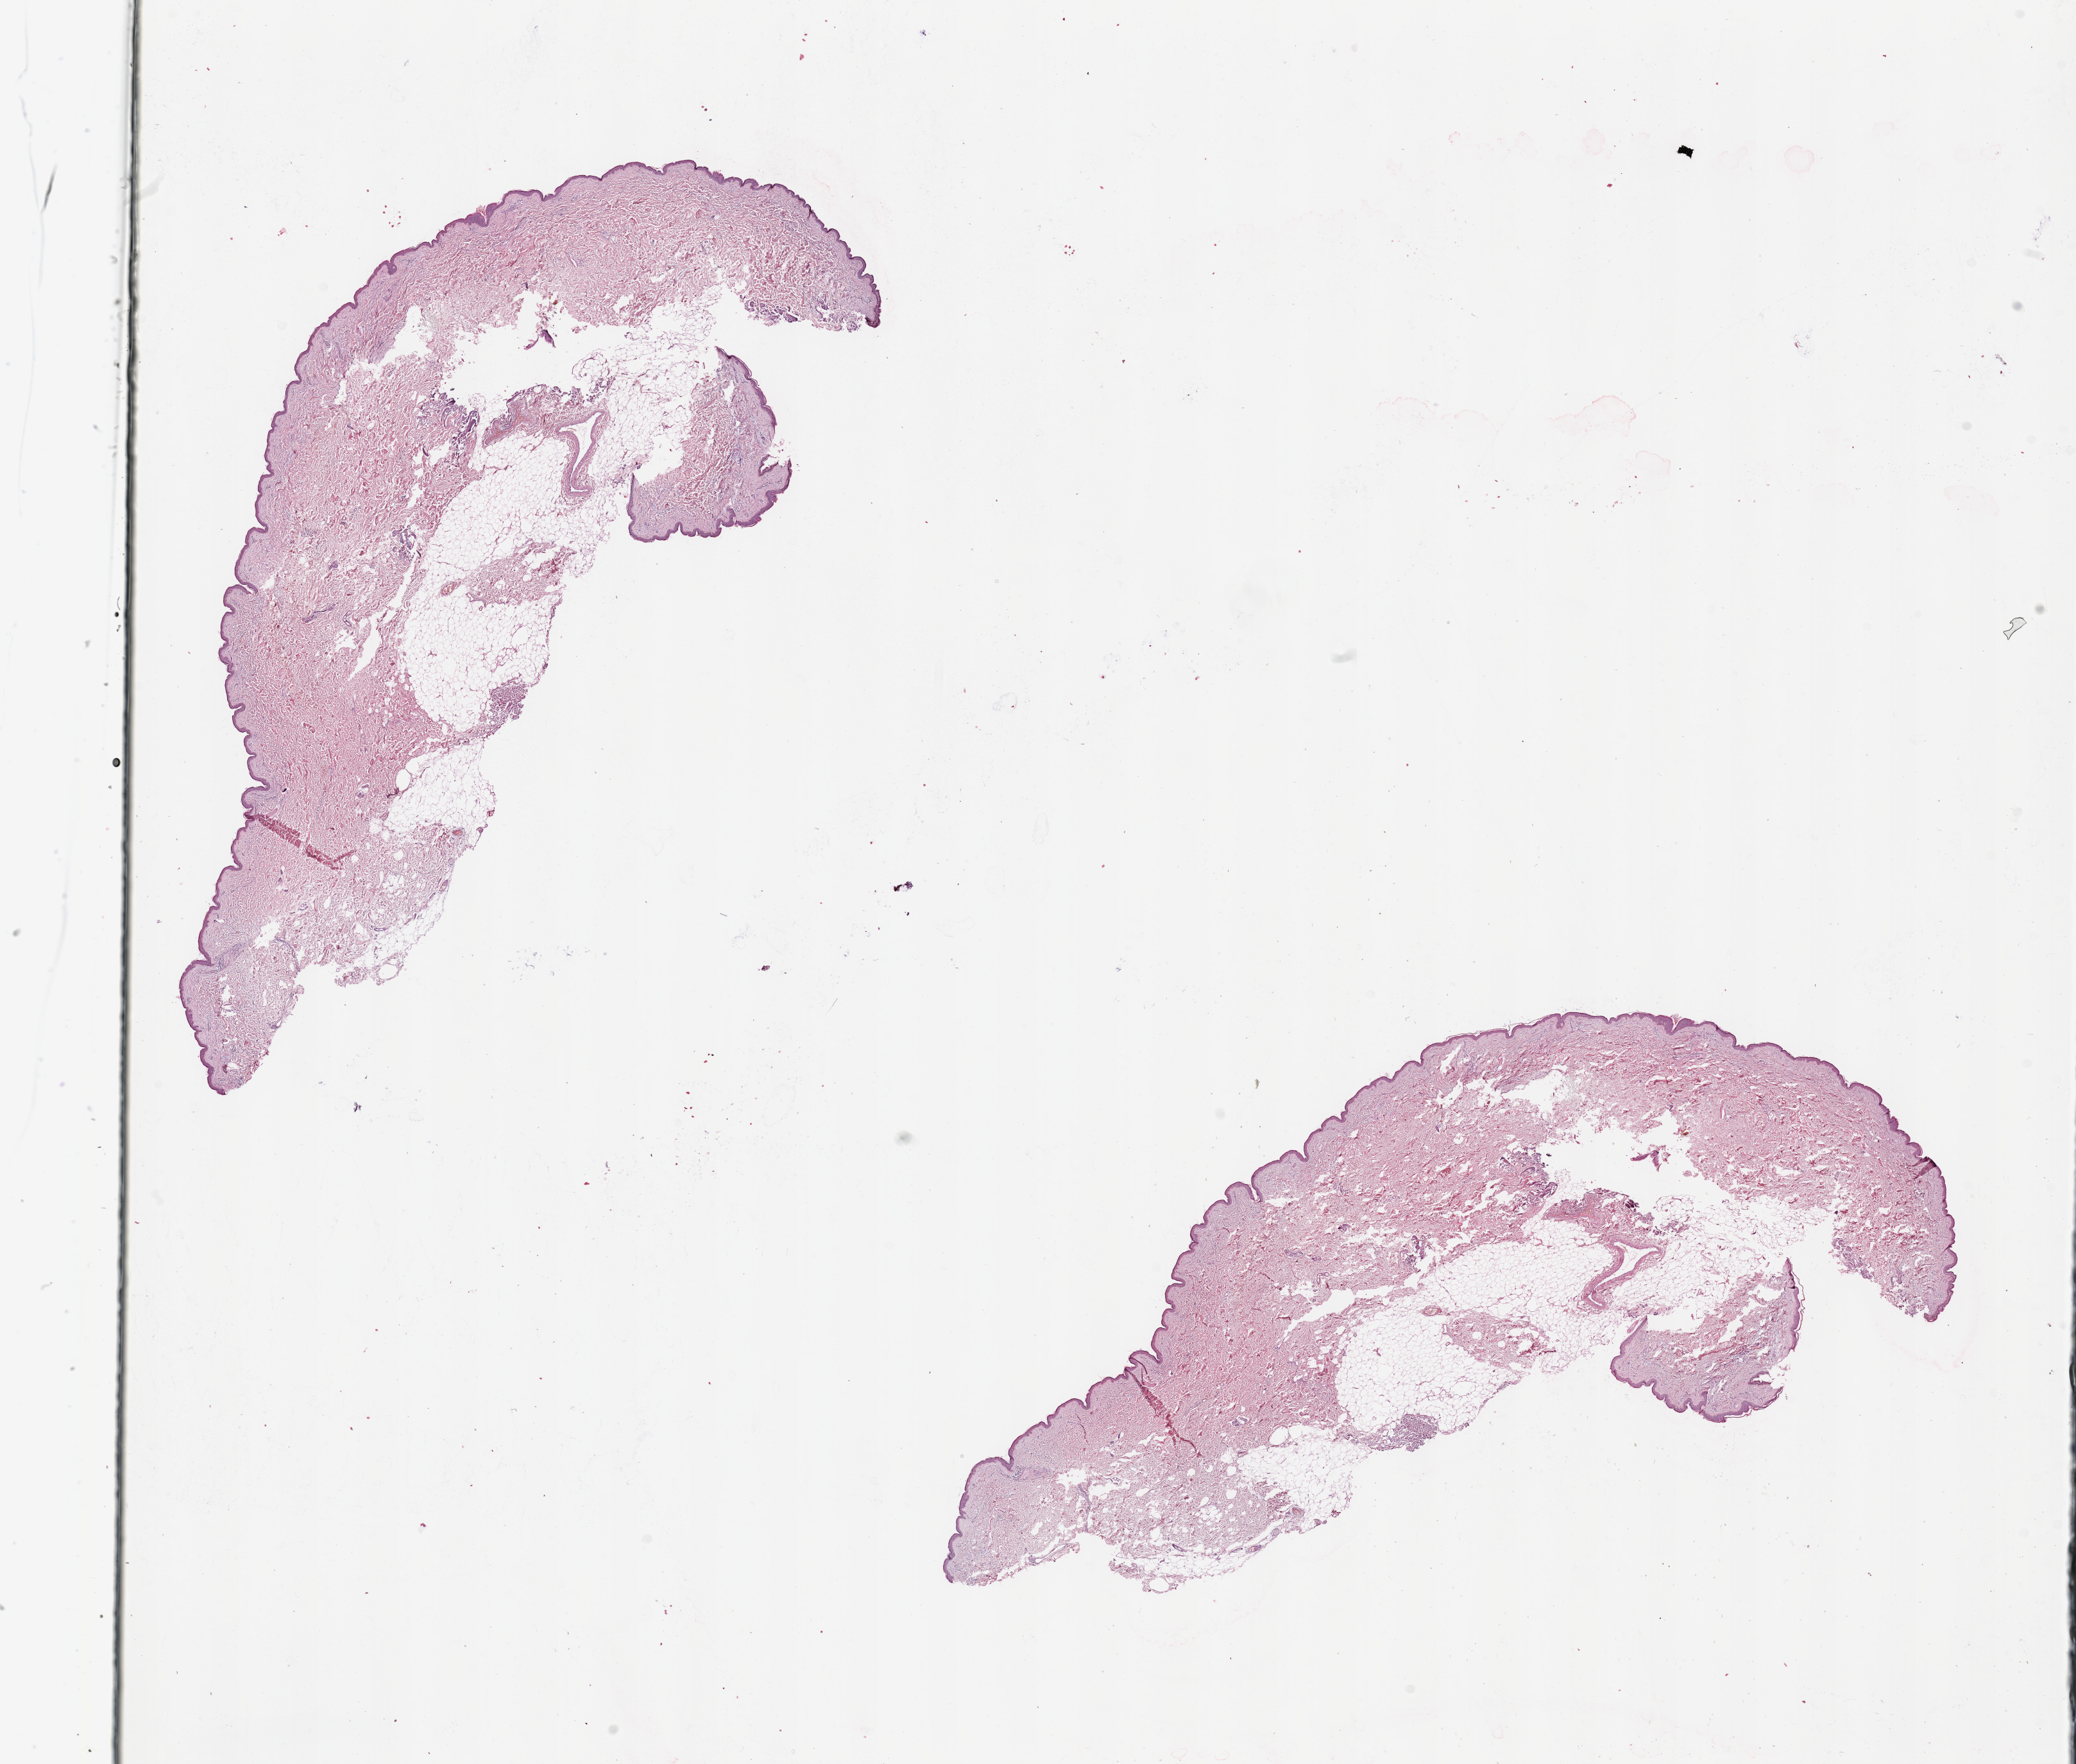
Digitized Hematoxylin and eosin (H&E) stained tissue section (whole slide), shown as a low-resolution overview of the whole scanned area (about 25.6 x 21.8 mm, slide scanned at 20x), normal (non-tumour) tissue sample. Female, 72 y/o.
This section: normal (non-tumour) tissue from the same patient. Patient diagnosis (cohort enrolment): sarcoma (site not recorded at cohort level).